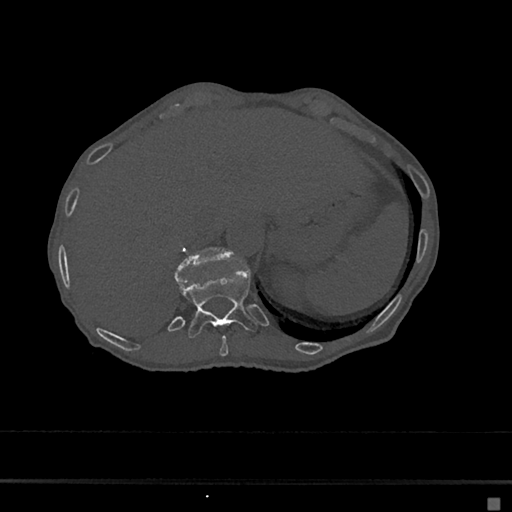
CT including the spine, one axial slice; position 176 of 797 along the scan axis; reconstruction kernel Br40s/3; bone window (W 1800 / L 400 HU); 0.5 mm slice thickness; 512 × 512 image matrix, field of view 360 × 360 mm. Patient: female, 68 years. From the clinical record (not read from this slice): primary cancer: renal.
Structures marked on this image (semi-automatically segmented with operator editing):
- T10 vertebra: box from (x=219, y=335) to (x=228, y=357) px
- T11 vertebra: (x=175, y=268)–(x=257, y=339)
- T12 vertebra: (x=175, y=247)–(x=232, y=275)